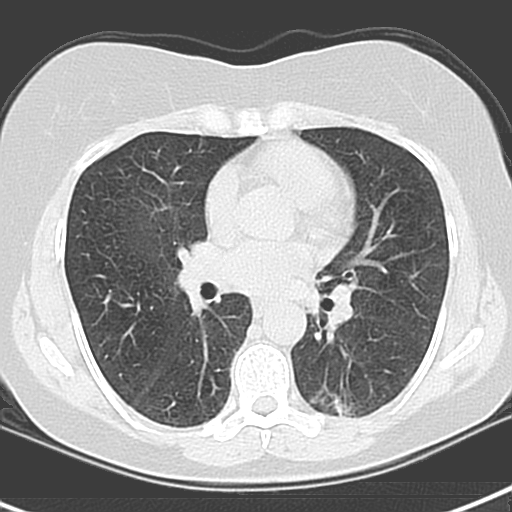
Axial slice from a low-dose chest CT screening exam, baseline screening round, lung window (W 1500 / L -600 HU), 120 kVp. Female participant, aged 55 years at enrolment. Current smoker at enrolment.
Expert-annotated lung lesion, bounding box <308,374,385,424> (left, top, right, bottom; pixels). The screening reader recorded 3 non-calcified nodules or masses ≥4 mm on this exam; which of them this box marks is not recorded. Official screen result: positive, change unspecified: nodule(s) >= 4 mm or enlarging nodule(s), mass(es), or other non-specific abnormalities suspicious for lung cancer. Participant outcome: lung cancer diagnosed 1063 days after this screen (after the third annual screen) — adenocarcinoma with mixed subtypes, left lower lobe, poorly differentiated (G3), stage IA (AJCC 6th edition), 21 mm at pathology.